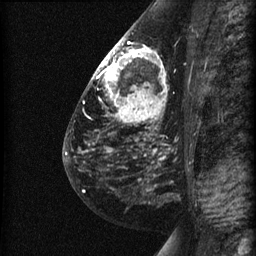
Breast MRI (dynamic contrast-enhanced), one sagittal slice; position 32 of 60 along the scan axis; dynamic contrast-enhanced series, image 2 of 3 at this slice position (ordered by acquisition); 1.5 T; TE 4.2 ms, TR 22.7 ms; 1.5 mm slice thickness; 256 × 256 image matrix, field of view 180 × 180 mm. Patient: female, 48 years. Case-level facts recorded for this patient, not image findings: setting: breast cancer imaged before/during neoadjuvant chemotherapy; receptor status: triple-negative.
Outlined on this slice (semi-automatic segmentation, software-assisted and operator-edited):
- analysis volume of interest (the breast-tissue region the enhancement analysis was run in; not a lesion): bounding box <89,27,191,180> (left, top, right, bottom; pixels)
- tumour enhancement mask (voxels above the 90 % enhancement threshold inside the analysis volume of interest): <94,38,165,117>